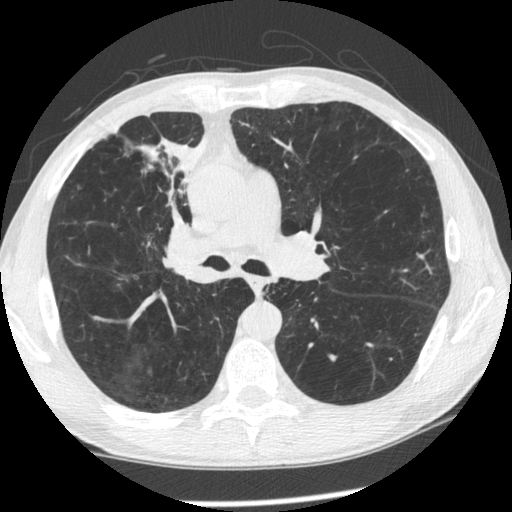
Low-dose screening chest CT, one axial slice. Position 142 of 261 along the scan axis. Lung window (W 1500 / L -600 HU). 512 × 512 image matrix.
Annotated regions visible in this slice (outlined manually by an expert reader):
- lesion 1 (tumor, upper lobe of right lung): bounding box <140,135,208,236> (left, top, right, bottom; pixels)